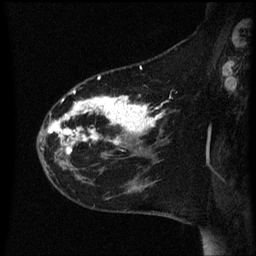
Breast MRI (dynamic contrast-enhanced), one sagittal slice; position 18 of 60 along the scan axis; dynamic contrast-enhanced series, image 2 of 3 at this slice position (ordered by acquisition); 1.5 T; TE 4.2 ms, TR 8.4 ms; 2.2 mm slice thickness; 256 × 256 image matrix, field of view 200 × 200 mm. Female patient, age 35 years. Case-level facts recorded for this patient, not image findings: setting: breast cancer imaged before/during neoadjuvant chemotherapy; receptor status: HER2-positive.
Structures marked on this image (semi-automatically segmented with operator editing):
- analysis volume of interest (the breast-tissue region the enhancement analysis was run in; not a lesion): bounding box <38,78,169,163> (left, top, right, bottom; pixels)
- tumour enhancement mask (voxels above the 70 % enhancement threshold inside the analysis volume of interest): <48,90,164,155>